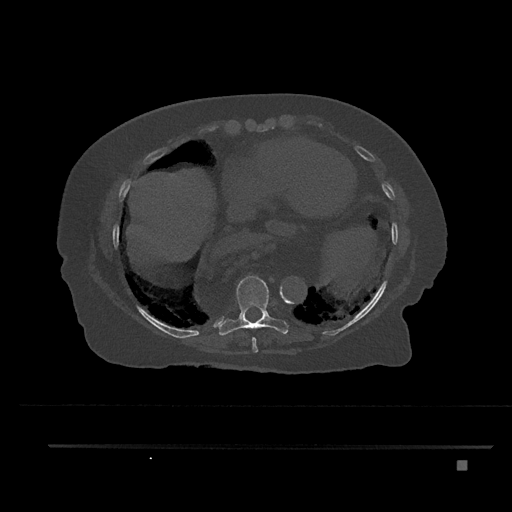
CT including the spine, one axial slice. Reconstruction kernel Br40s/3. Bone window (W 1800 / L 400 HU). 0.5 mm slice thickness. 512 × 512 image matrix. Patient: female, 76 years. Case-level facts recorded for this patient, not image findings: primary cancer: lung.
Annotated regions visible in this slice (semi-automatic segmentation, software-assisted and operator-edited):
- T8 vertebra: box from (x=252, y=337) to (x=258, y=353) px
- T9 vertebra: (x=217, y=276)–(x=289, y=336)